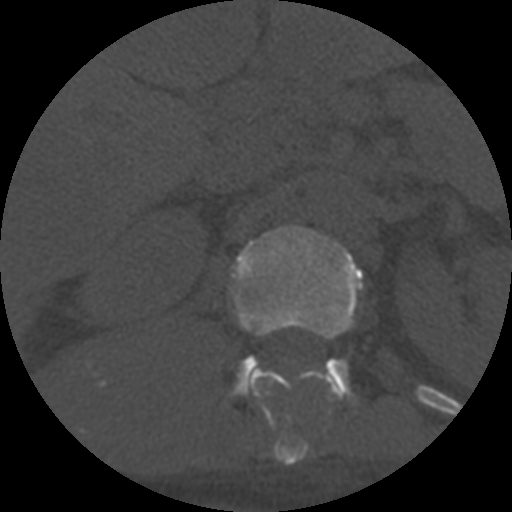
CT including the spine, one axial slice; position 300 of 708 along the scan axis; reconstruction kernel STANDARD; one of 3 acquisitions stored at this slice position; bone window (W 1800 / L 400 HU); 1.25 mm slice thickness; 512 × 512 image matrix, field of view 160 × 160 mm. Patient age 55 years. From the clinical record (not read from this slice): primary cancer: colon; vertebrae with lytic lesions (as recorded): T12, L1, L5.
Annotated regions visible in this slice (semi-automatically segmented with operator editing):
- L1 vertebra: box from (x=233, y=226) to (x=363, y=400) px
- T12 vertebra: (x=249, y=370)–(x=331, y=465)